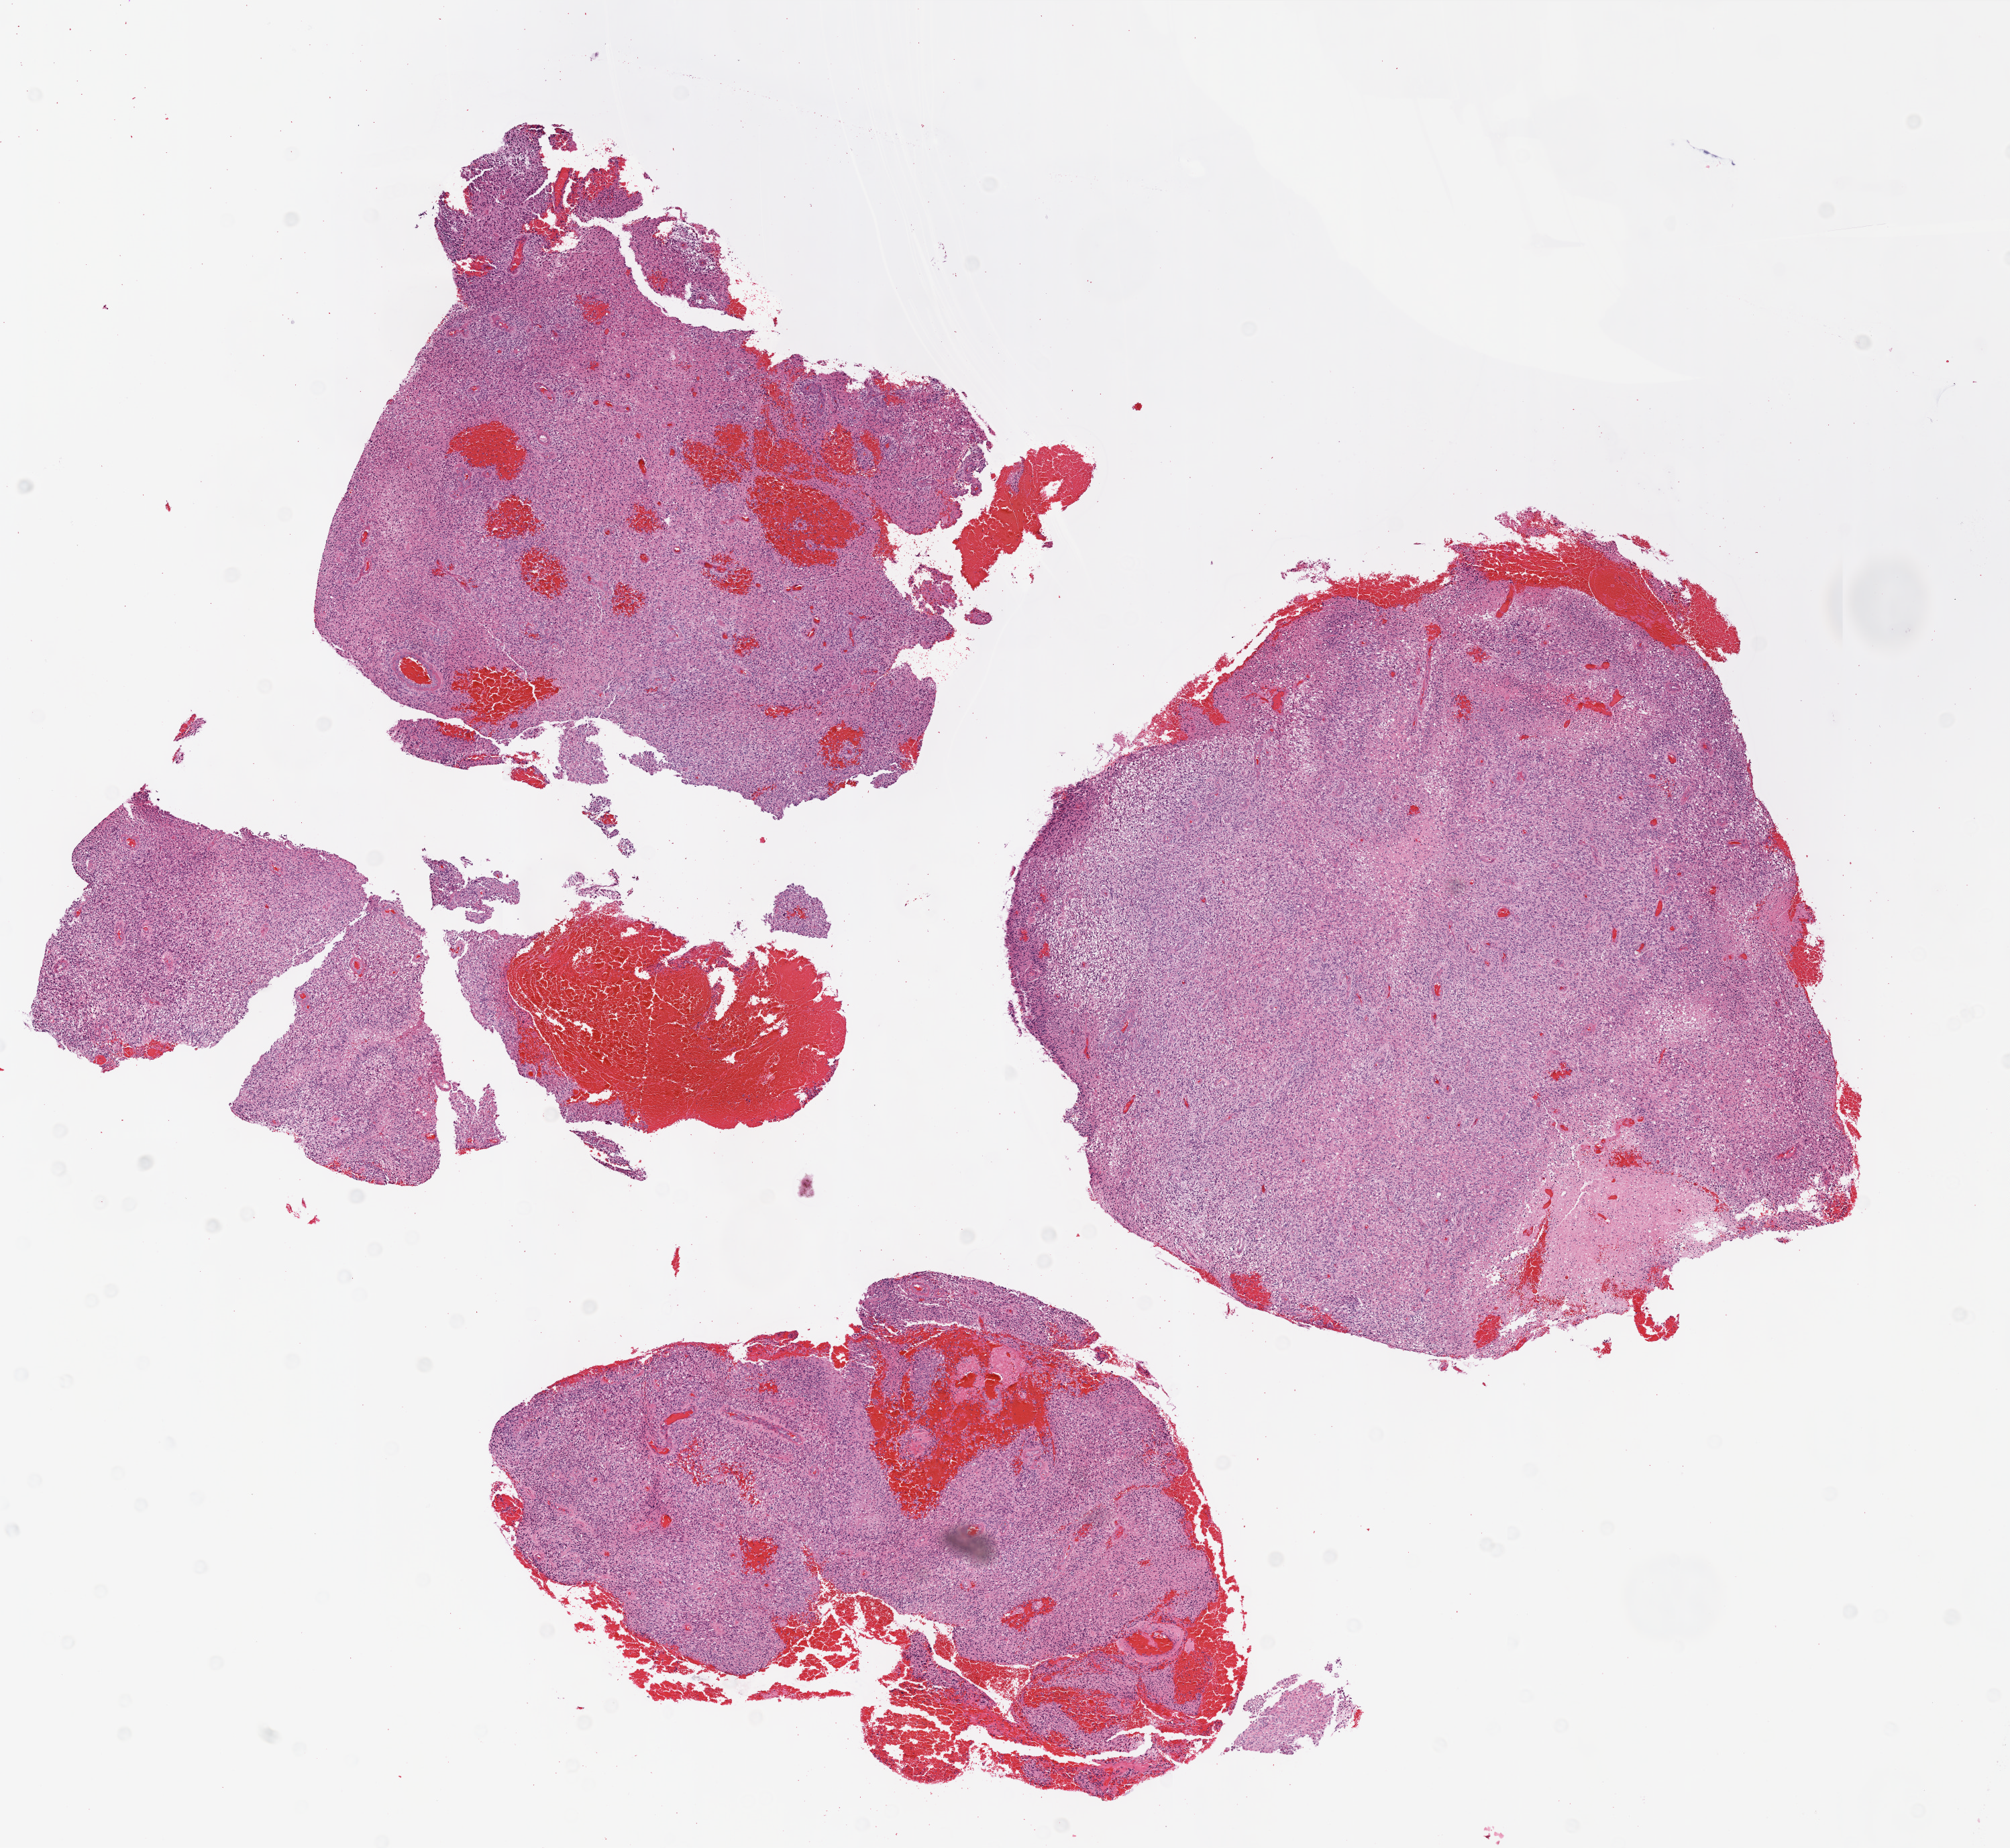
Whole-slide histology image, Hematoxylin and eosin (H&E) stained, shown as a low-resolution overview of the whole scanned area (about 12.0 x 11.0 mm), formalin-fixed paraffin-embedded (FFPE) diagnostic section, sample: primary tumour, brain. Female, age 72 years at initial diagnosis.
Histologic diagnosis: Glioblastoma.